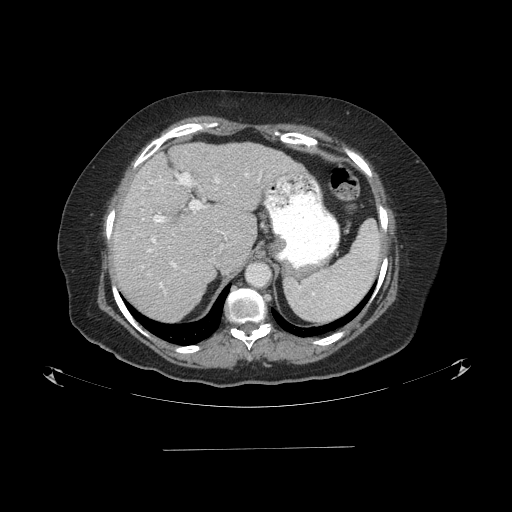
Contrast-enhanced abdominal CT (liver protocol), one axial slice. Slice 63 of 103 in the series (ordered by position). Reconstruction kernel STANDARD. One of 2 acquisitions stored at this slice position. Soft-tissue window (W 400 / L 40 HU). 2.5 mm slice thickness. 512 × 512 image matrix. From the clinical record (not read from this slice): diagnosis: hepatocellular carcinoma (patient treated with transarterial chemoembolisation; whether this scan precedes or follows treatment is not stated here); TNM stage (as recorded): Stage-IIIA.
Annotated regions visible in this slice (semi-automatically segmented with operator editing):
- abdominal aorta: bounding box <248,263,271,286> (left, top, right, bottom; pixels)
- liver parenchyma outside the tumour (the mass and vessels are separate outlines, so this box may not span the whole liver): <112,142,304,320>
- liver vessels: <143,172,259,288>